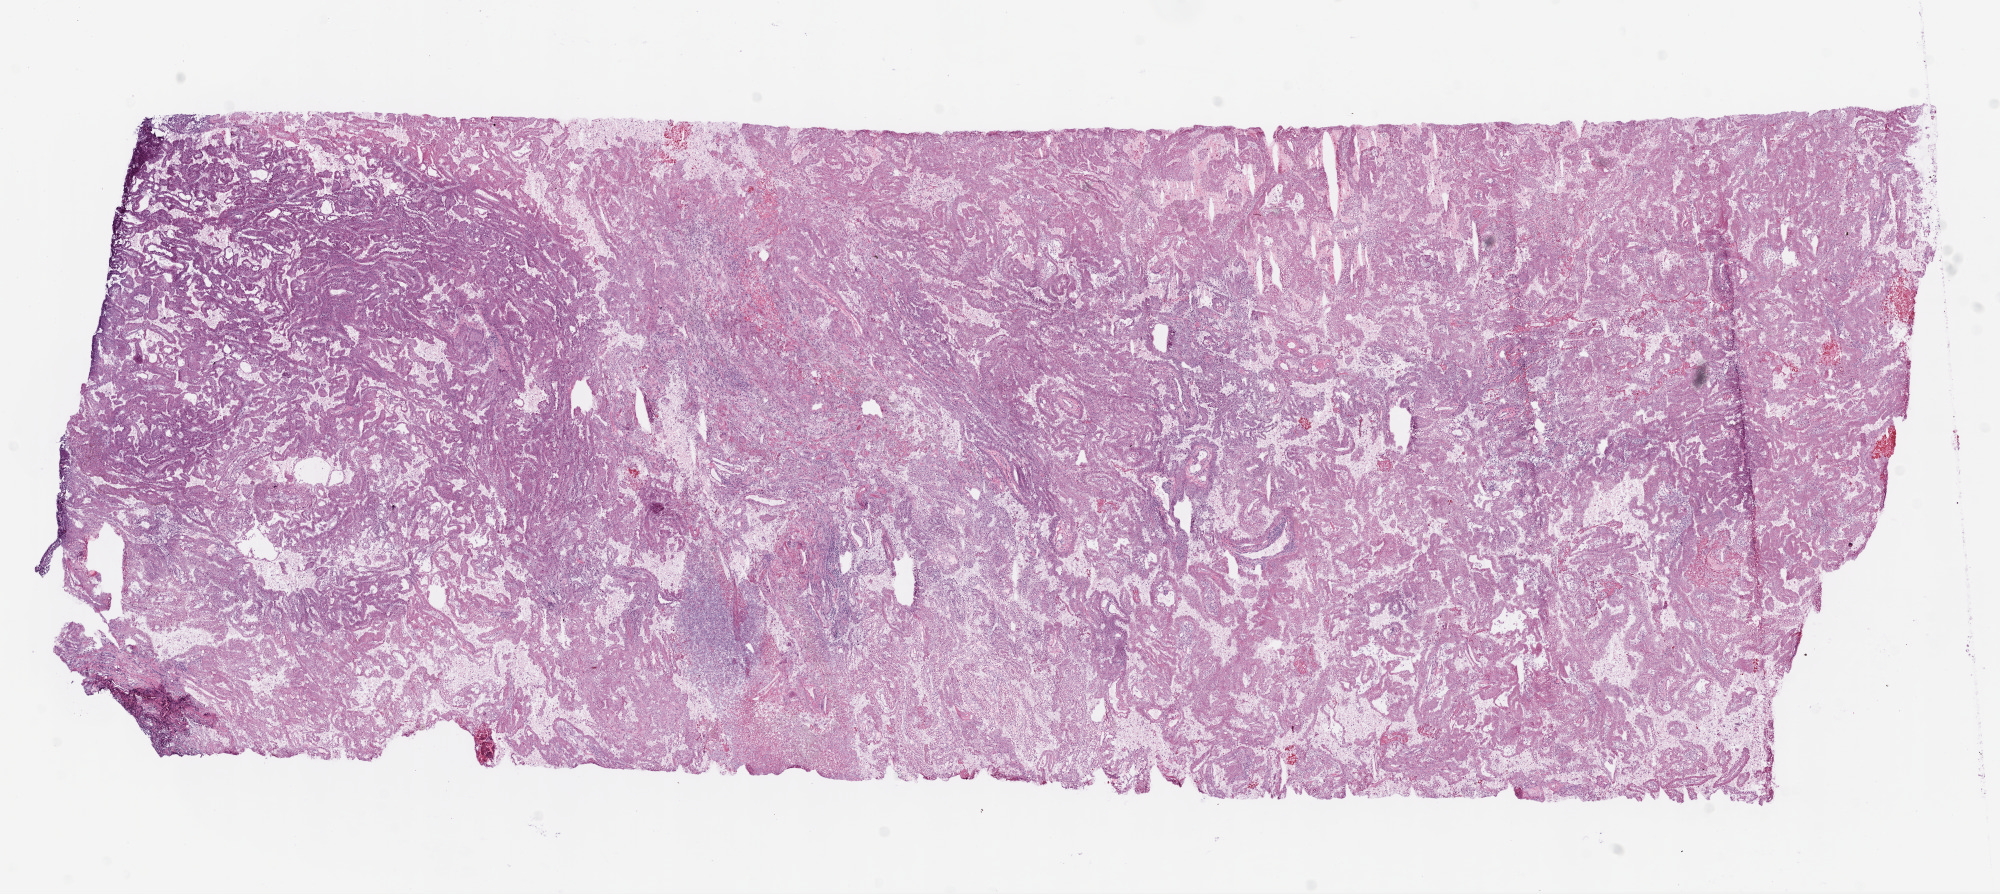
Whole-slide histology image, H&E — a low-resolution overview of the entire scanned area, about 16.0 x 7.2 mm. Frozen section from the top of the tissue portion. Kidney, primary tumour sample. Female patient; age at initial diagnosis 72 years. Histologic grade: G2 (moderately differentiated). Composition of this section per pathologist review: tumour cells 95%, tumour nuclei 85%, normal cells 0%, stromal cells 0%, necrosis 5%. Inflammatory infiltration, as recorded: lymphocyte infiltration 9%, monocyte infiltration 0%, neutrophil infiltration 0%.
Laterality: left. AJCC pathologic stage: I. Pathologic diagnosis: Clear cell adenocarcinoma, NOS. TNM: T1b NX M0.